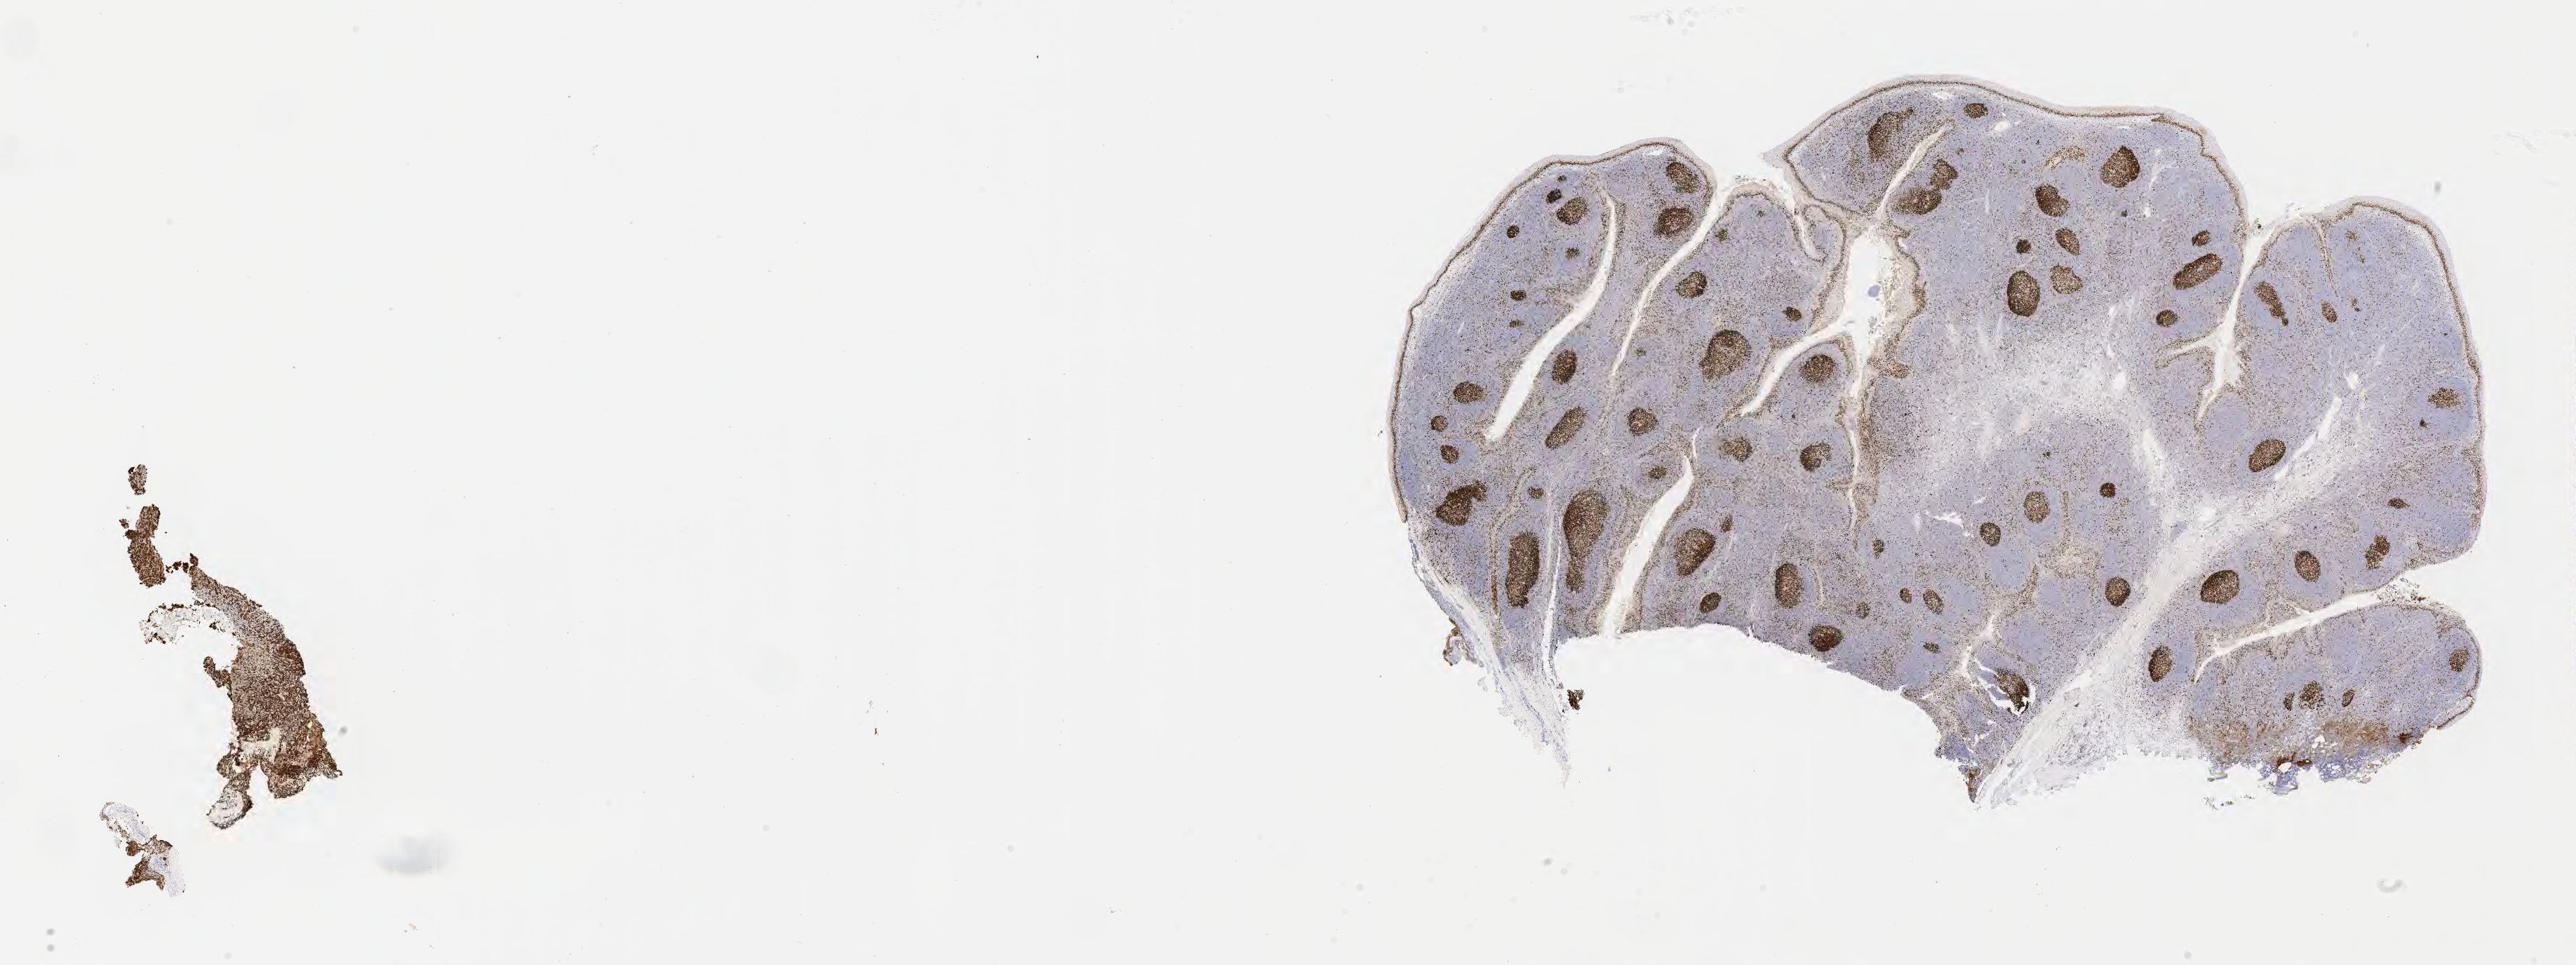
Immunohistochemistry (IHC) whole-slide image stained for Ki-67, whole scanned area (about 29.7 x 11.1 mm) shown as a low-resolution overview, specimen: tumor tissue. Female patient, 27 years old.
* histologic diagnosis: Diffuse large B-cell lymphoma, NOS